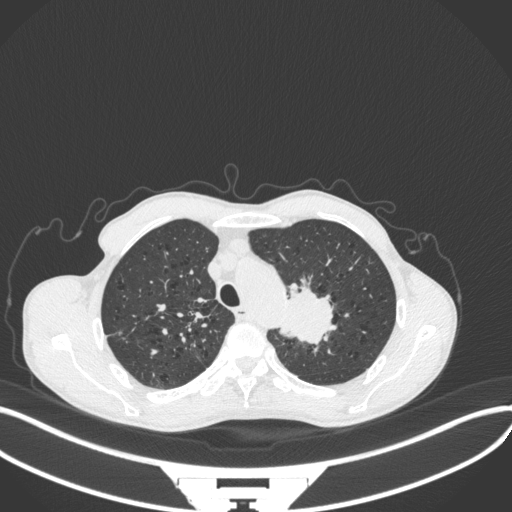
Chest CT, one axial slice; position 329 of 394 along the scan axis; lung window (W 1500 / L -600 HU); 1 mm slice thickness; 512 × 512 image matrix, field of view 400 × 400 mm. Male patient, age 65 years. From the clinical record (not read from this slice): clinical TNM (as recorded): T2b N0 M0; histopathological grade: G2.
Outlined on this slice (rectangle marked by the reading radiologist):
- lung tumour (recorded histology: adenocarcinoma): bounding box [x1, y1, x2, y2] px = [271, 268, 340, 350]